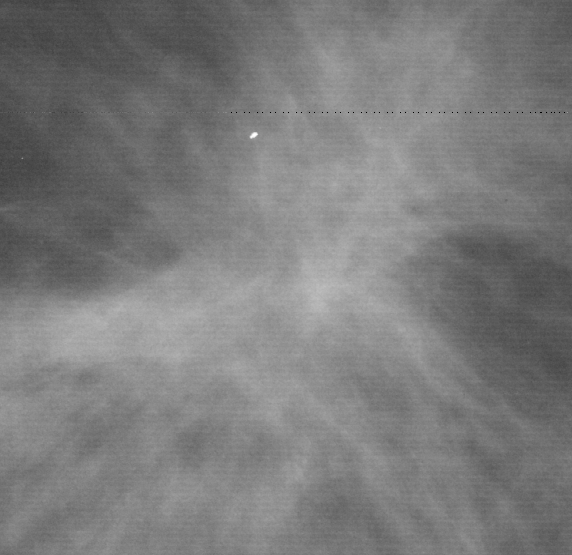
Cropped region of a digitized screen-film mammogram centred on a radiologist-marked abnormality, right breast, CC view, BI-RADS breast density category 2 (scale 1–4).
Finding: mass, shape architectural distortion, margins spiculated; BI-RADS assessment category 2; pathology (as recorded): benign.